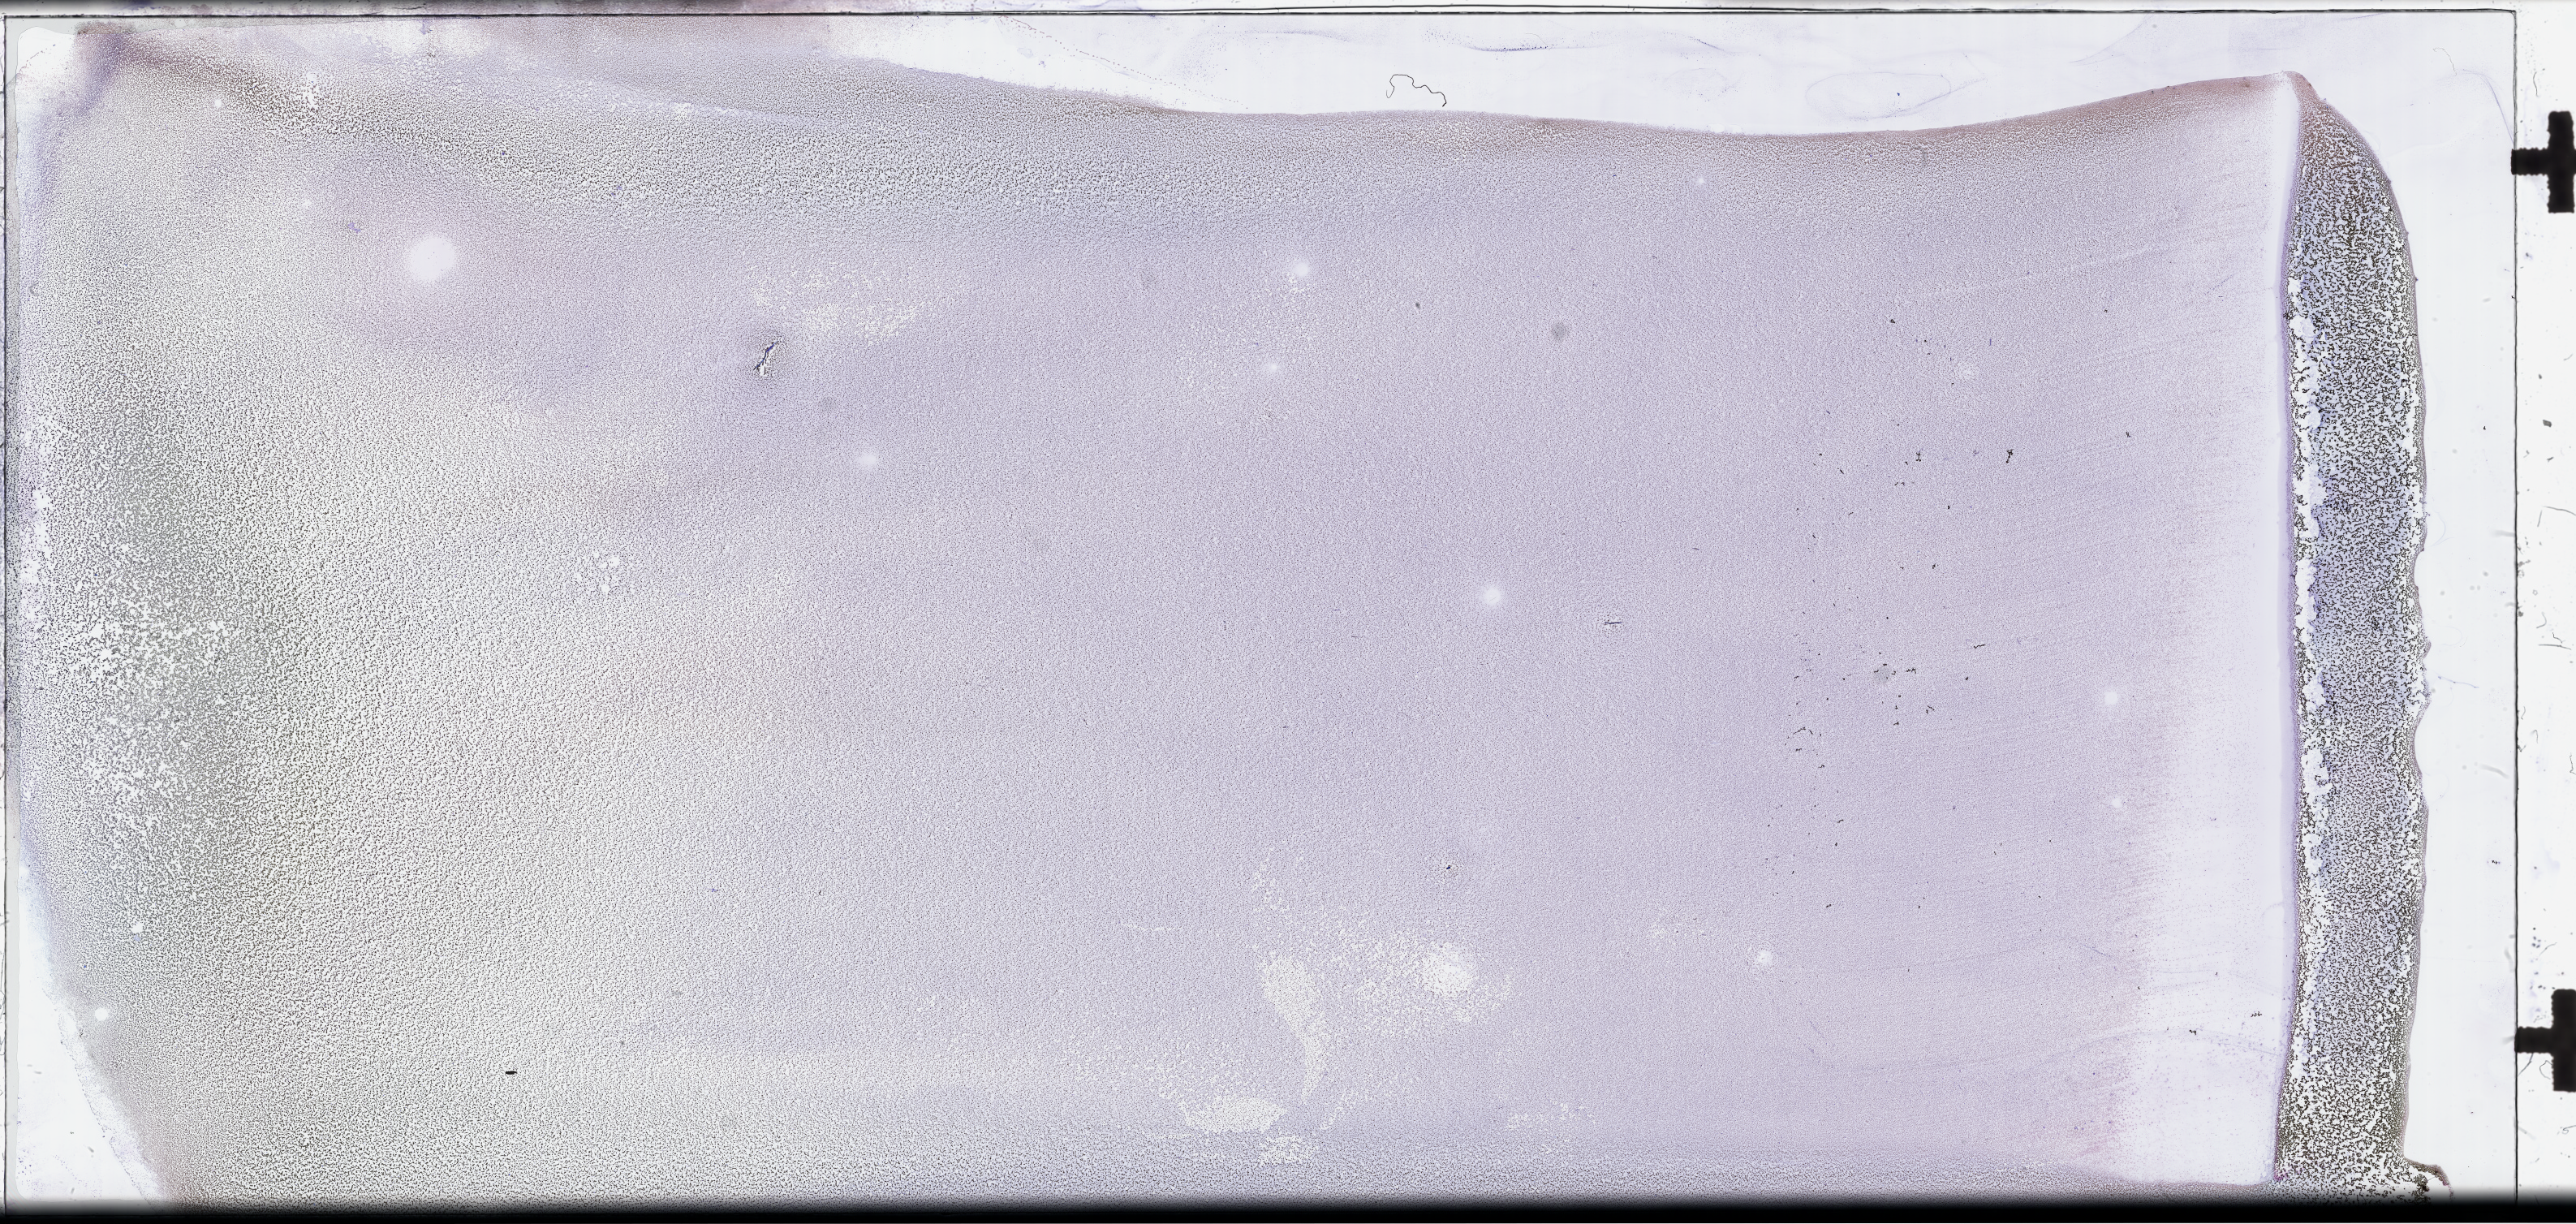
Whole-slide image of a bone marrow smear, Wright-Giemsa stain, whole scanned area (about 51.3 x 24.4 mm) shown as a low-resolution overview, specimen time point: collected at baseline (before treatment). Male patient.
Patient diagnosis: Plasma Cell Myeloma.